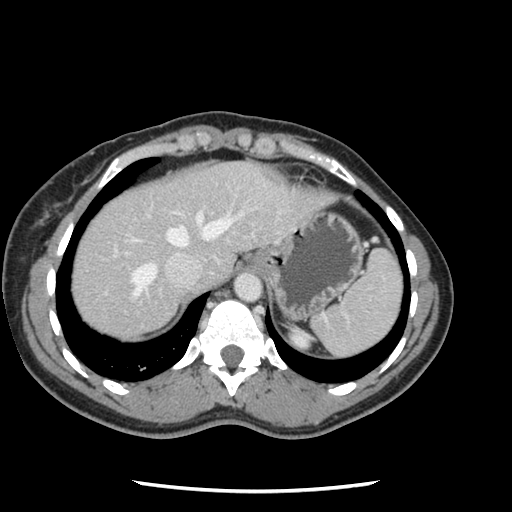
Contrast-enhanced abdominal CT, one axial slice. Slice 101 of 134 in the series (ordered by position). 120 kVp. Intravenous contrast given. Soft-tissue window (W 400 / L 40 HU). 2.5 mm slice thickness. 512 × 512 image matrix, field of view 330 × 330 mm. Female patient, age 43 years. From the clinical record (not read from this slice): diagnosis: colorectal cancer liver metastases, imaged before liver resection; multiple liver metastases: yes; largest metastasis: 3.4 cm.
Outlined on this slice (manually delineated by an expert):
- hepatic veins: box from (x=132, y=211) to (x=242, y=298) px
- liver: (x=71, y=161)–(x=324, y=339)
- planned liver remnant (the part of the liver to remain after resection): (x=71, y=175)–(x=198, y=306)
- portal vein (with intrahepatic branches): (x=114, y=245)–(x=131, y=258)